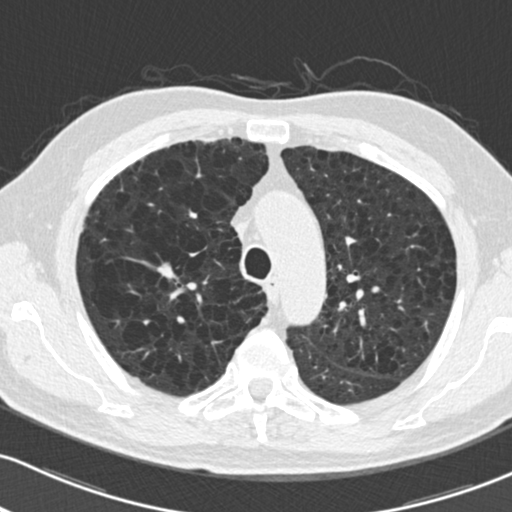
Low-dose screening chest CT, one axial slice. Slice 154 of 204 in the series (ordered by position). Lung window (W 1500 / L -600 HU). 2 mm slice thickness. 512 × 512 image matrix.
Structures marked on this image (manually delineated by an expert):
- lesion 1 (tumor, upper lobe of right lung): box from (x=157, y=263) to (x=175, y=279) px